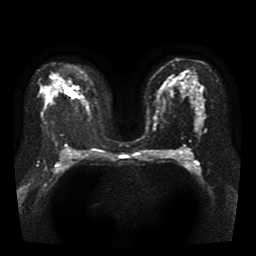
Breast MRI, one axial slice; position 25 of 41 along the scan axis; diffusion-weighted series; image 2 of 4 stored at this slice position (different b-values; order by instance number); 1.5 T; 5 mm slice thickness; 256 × 256 image matrix. Female patient.
Outlined on this slice (expert manual segmentation):
- tumour on diffusion-weighted imaging: bounding box (x1, y1, x2, y2) in pixels: (65, 88, 76, 98)